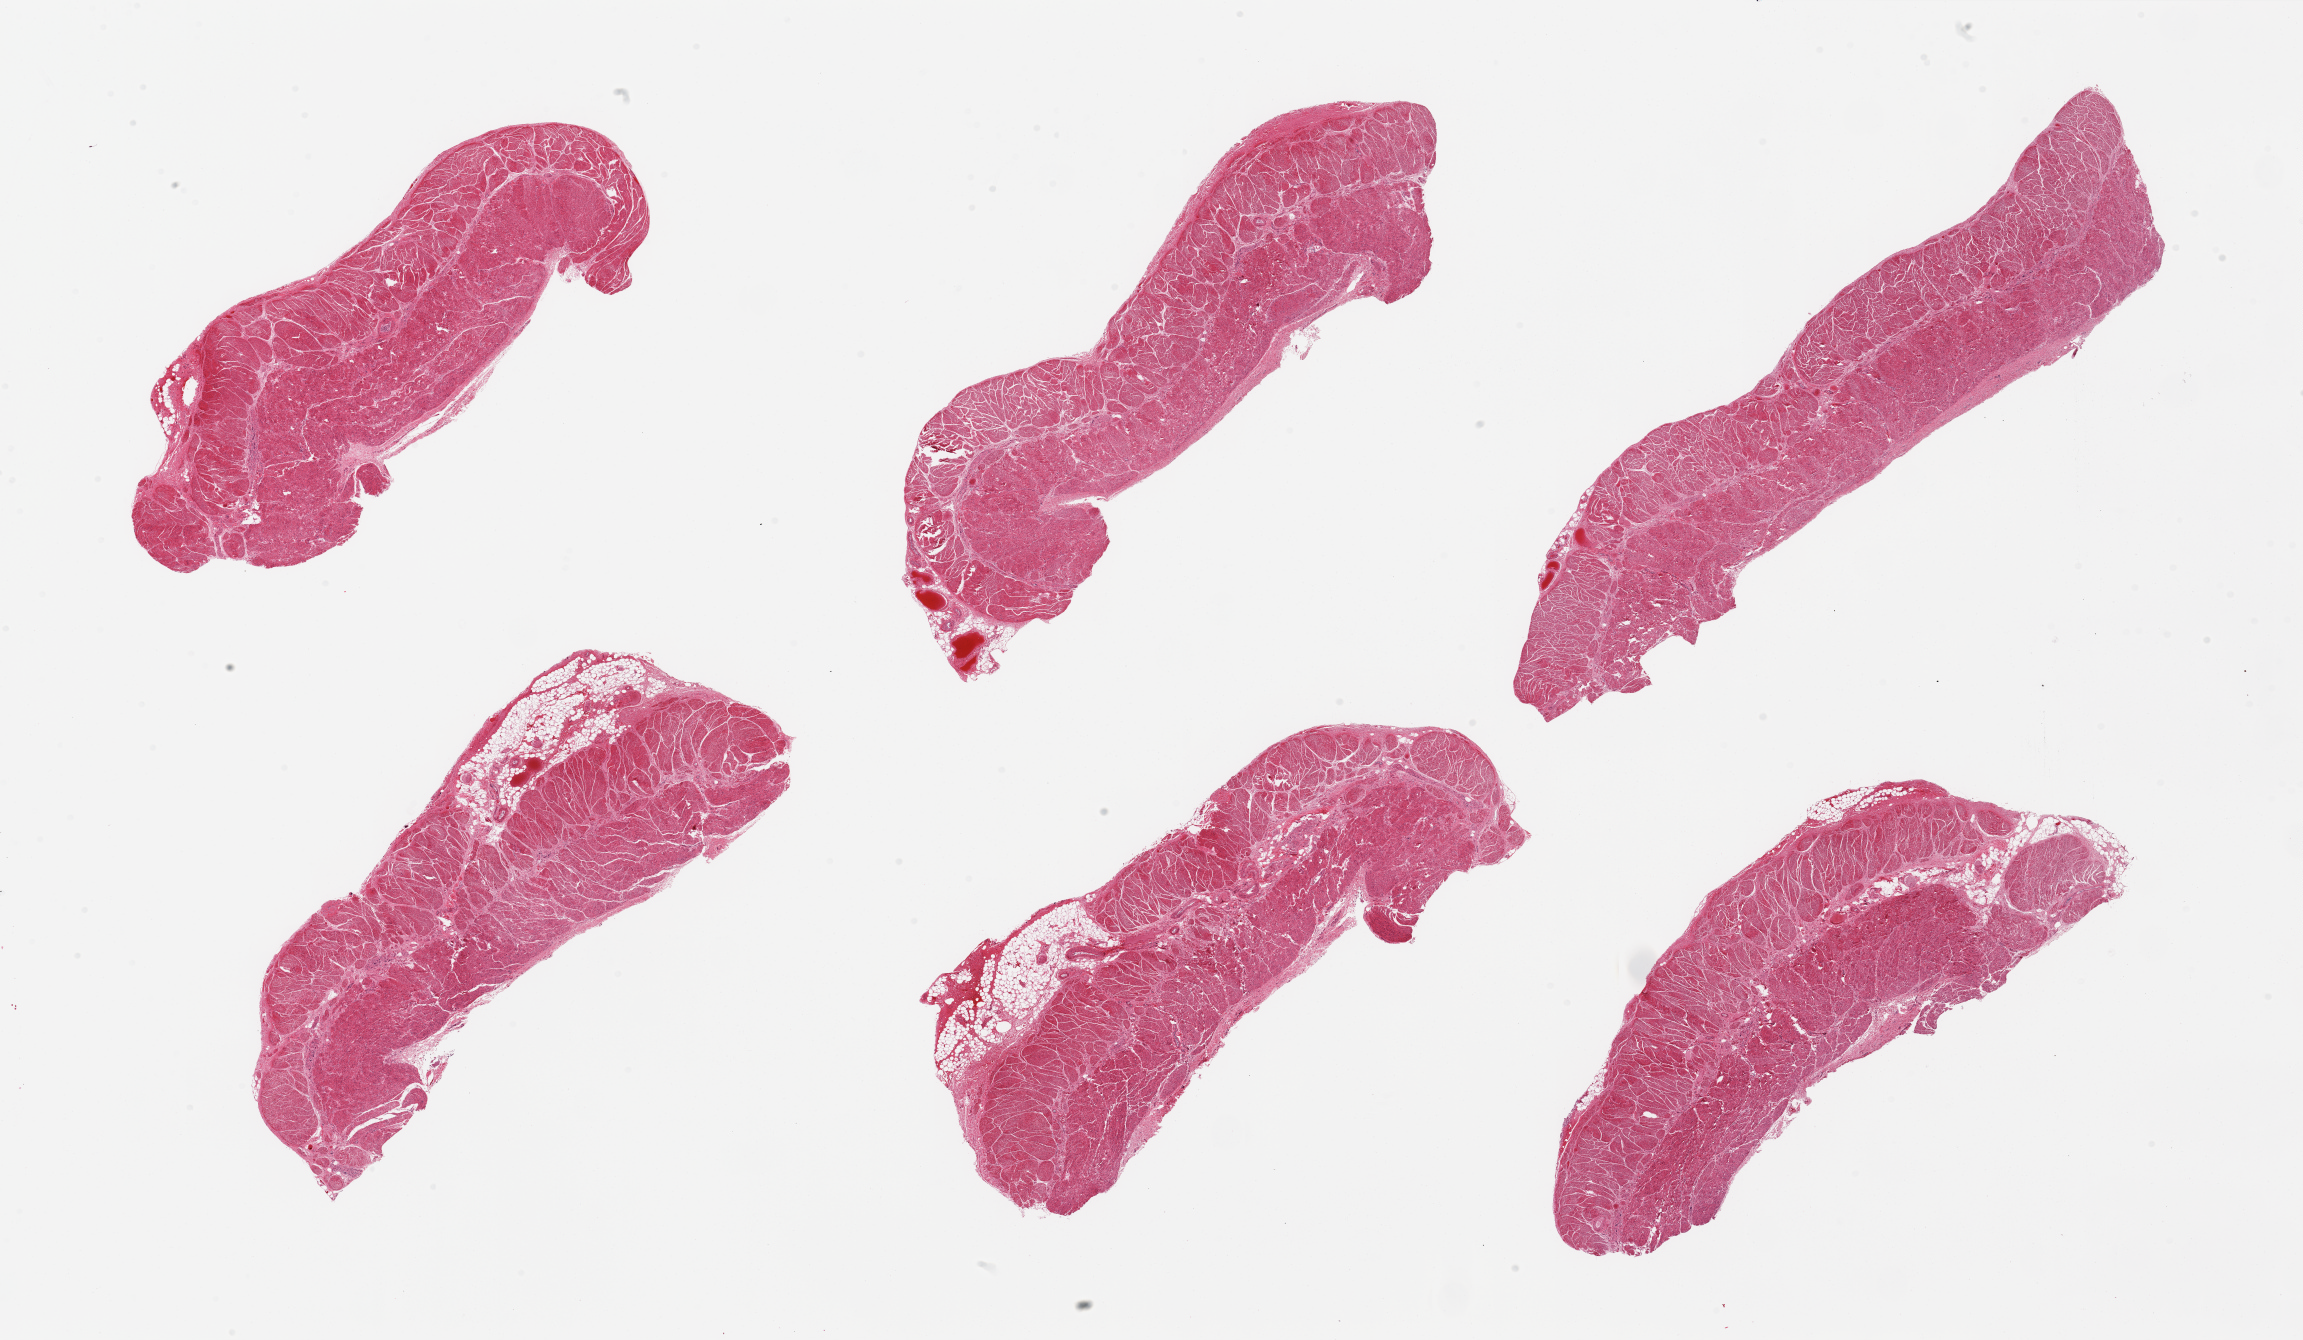
Hematoxylin and eosin (H&E) whole-slide image, low-resolution overview of the scanned area, about 36.4 x 21.2 mm; PAXgene-fixed, paraffin-embedded tissue; section of gastroesophageal junction (target tissue); donor tissue sample. Male donor.
Reviewer comment on this tissue sample: 6 pieces; few sections with ~15% fat.